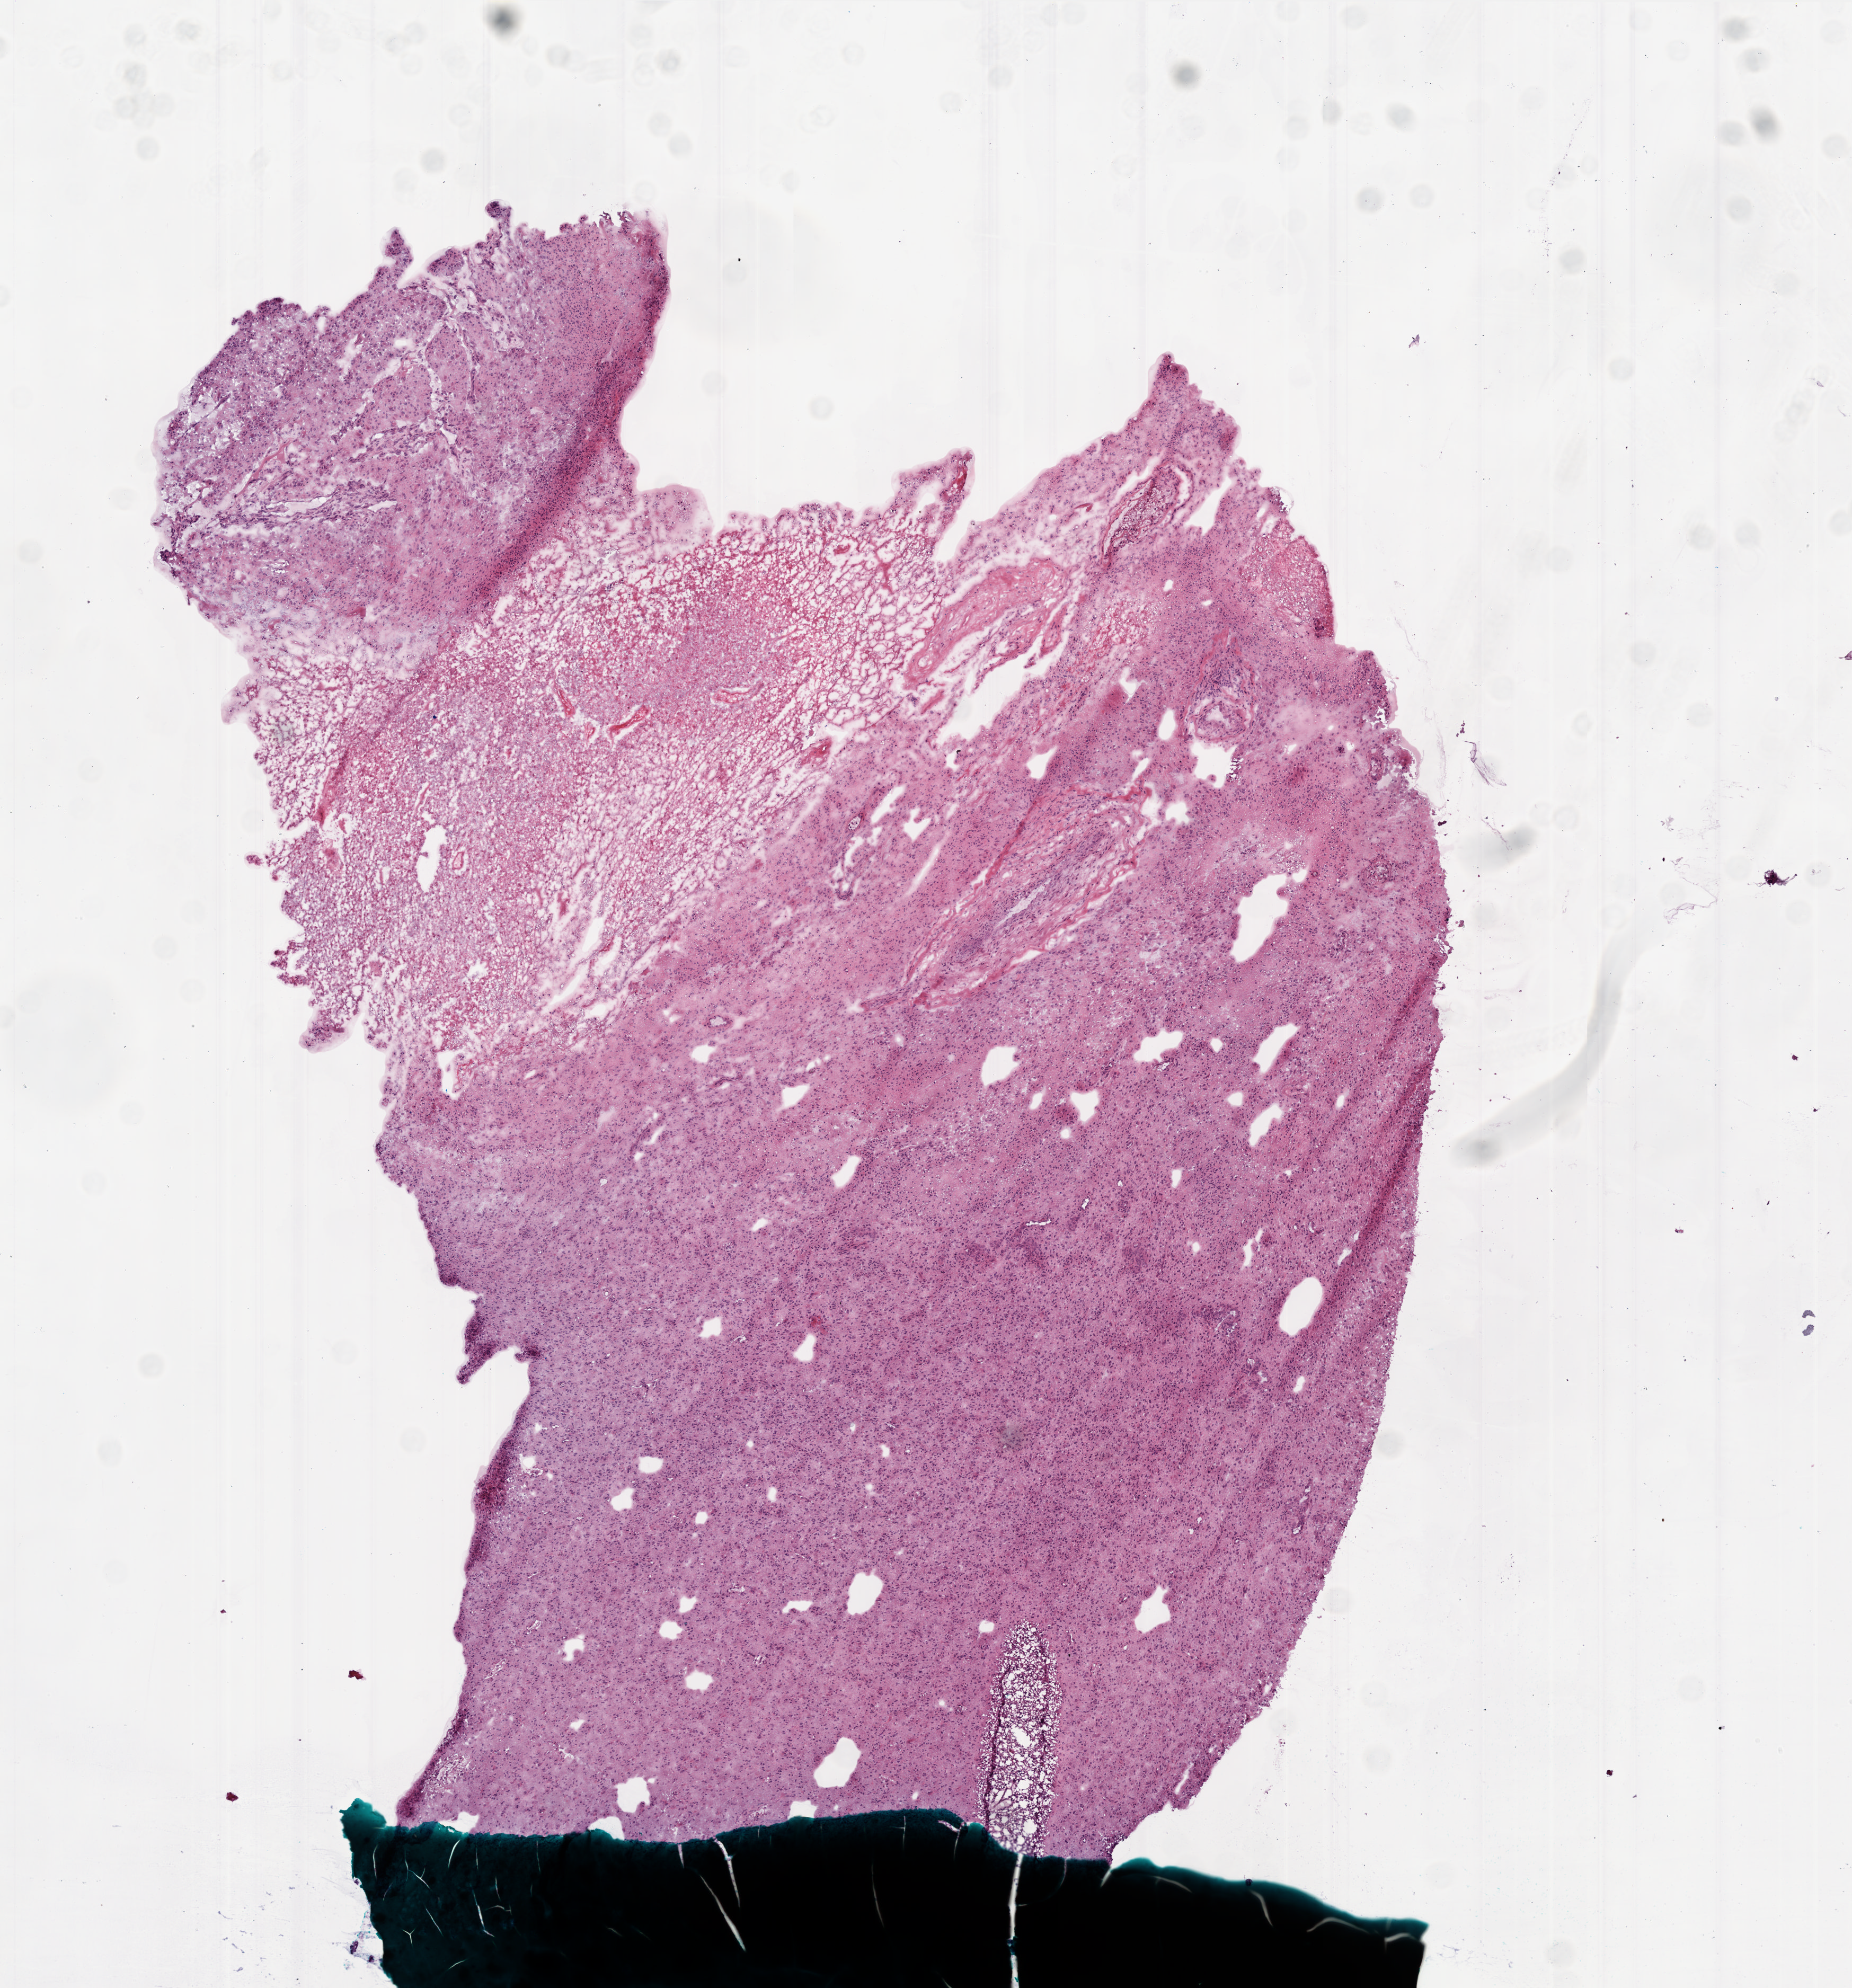
Whole-slide histology image, H&E — shown as a low-resolution overview of the whole scanned area (about 7.0 x 7.5 mm, acquisition: 20x scan). Frozen section from the bottom of the tissue portion. Sample: primary tumour, brain. Male patient; age at initial diagnosis 50 years. Pathologist review of this section (percent, as recorded): tumour cells 75%, tumour nuclei 100%, normal cells 0%, stromal cells 0%, necrosis 25%. Inflammatory infiltration, as recorded: lymphocyte infiltration 0%.
Pathologic diagnosis: Glioblastoma.